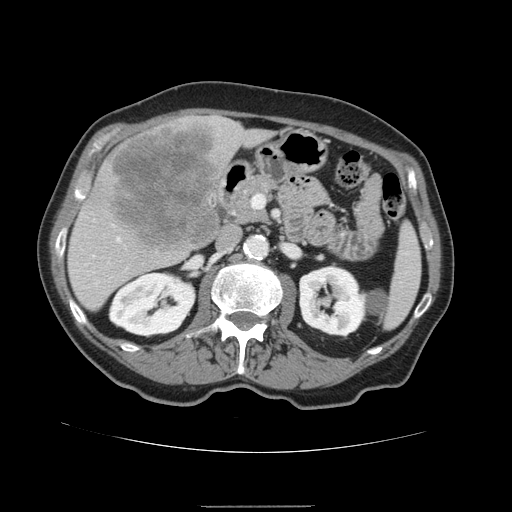
Contrast-enhanced abdominal CT, one axial slice; slice 71 of 168 in the series (ordered by position); 120 kVp; intravenous contrast given; soft-tissue window (W 400 / L 40 HU); 512 × 512 image matrix. Male patient, age 74 years. From the clinical record (not read from this slice): diagnosis: colorectal cancer liver metastases, imaged before liver resection; multiple liver metastases: no; largest metastasis: 14.5 cm; chemotherapy before resection: no.
Annotated regions visible in this slice (manually delineated by an expert):
- liver: bounding box (x1, y1, x2, y2) in pixels: (67, 115, 276, 312)
- planned liver remnant (the part of the liver to remain after resection): (69, 128, 276, 311)
- liver metastasis: (113, 122, 220, 250)